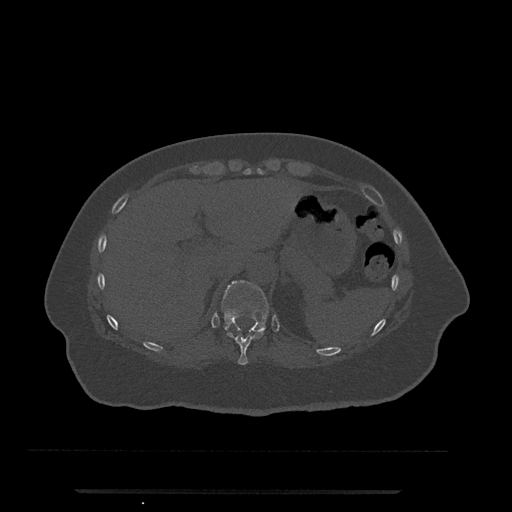
CT including the spine, one axial slice; slice 254 of 797 in the series (ordered by position); bone window (W 1800 / L 400 HU); 0.5 mm slice thickness; 512 × 512 image matrix, field of view 440 × 440 mm. Patient: female, 51 years. From the clinical record (not read from this slice): primary cancer: neuro; vertebrae with lytic lesions (as recorded): T8.
Outlined on this slice (semi-automatically segmented with operator editing):
- T10 vertebra: bounding box (x1, y1, x2, y2) in pixels: (226, 329, 265, 365)
- T11 vertebra: (222, 280, 269, 334)